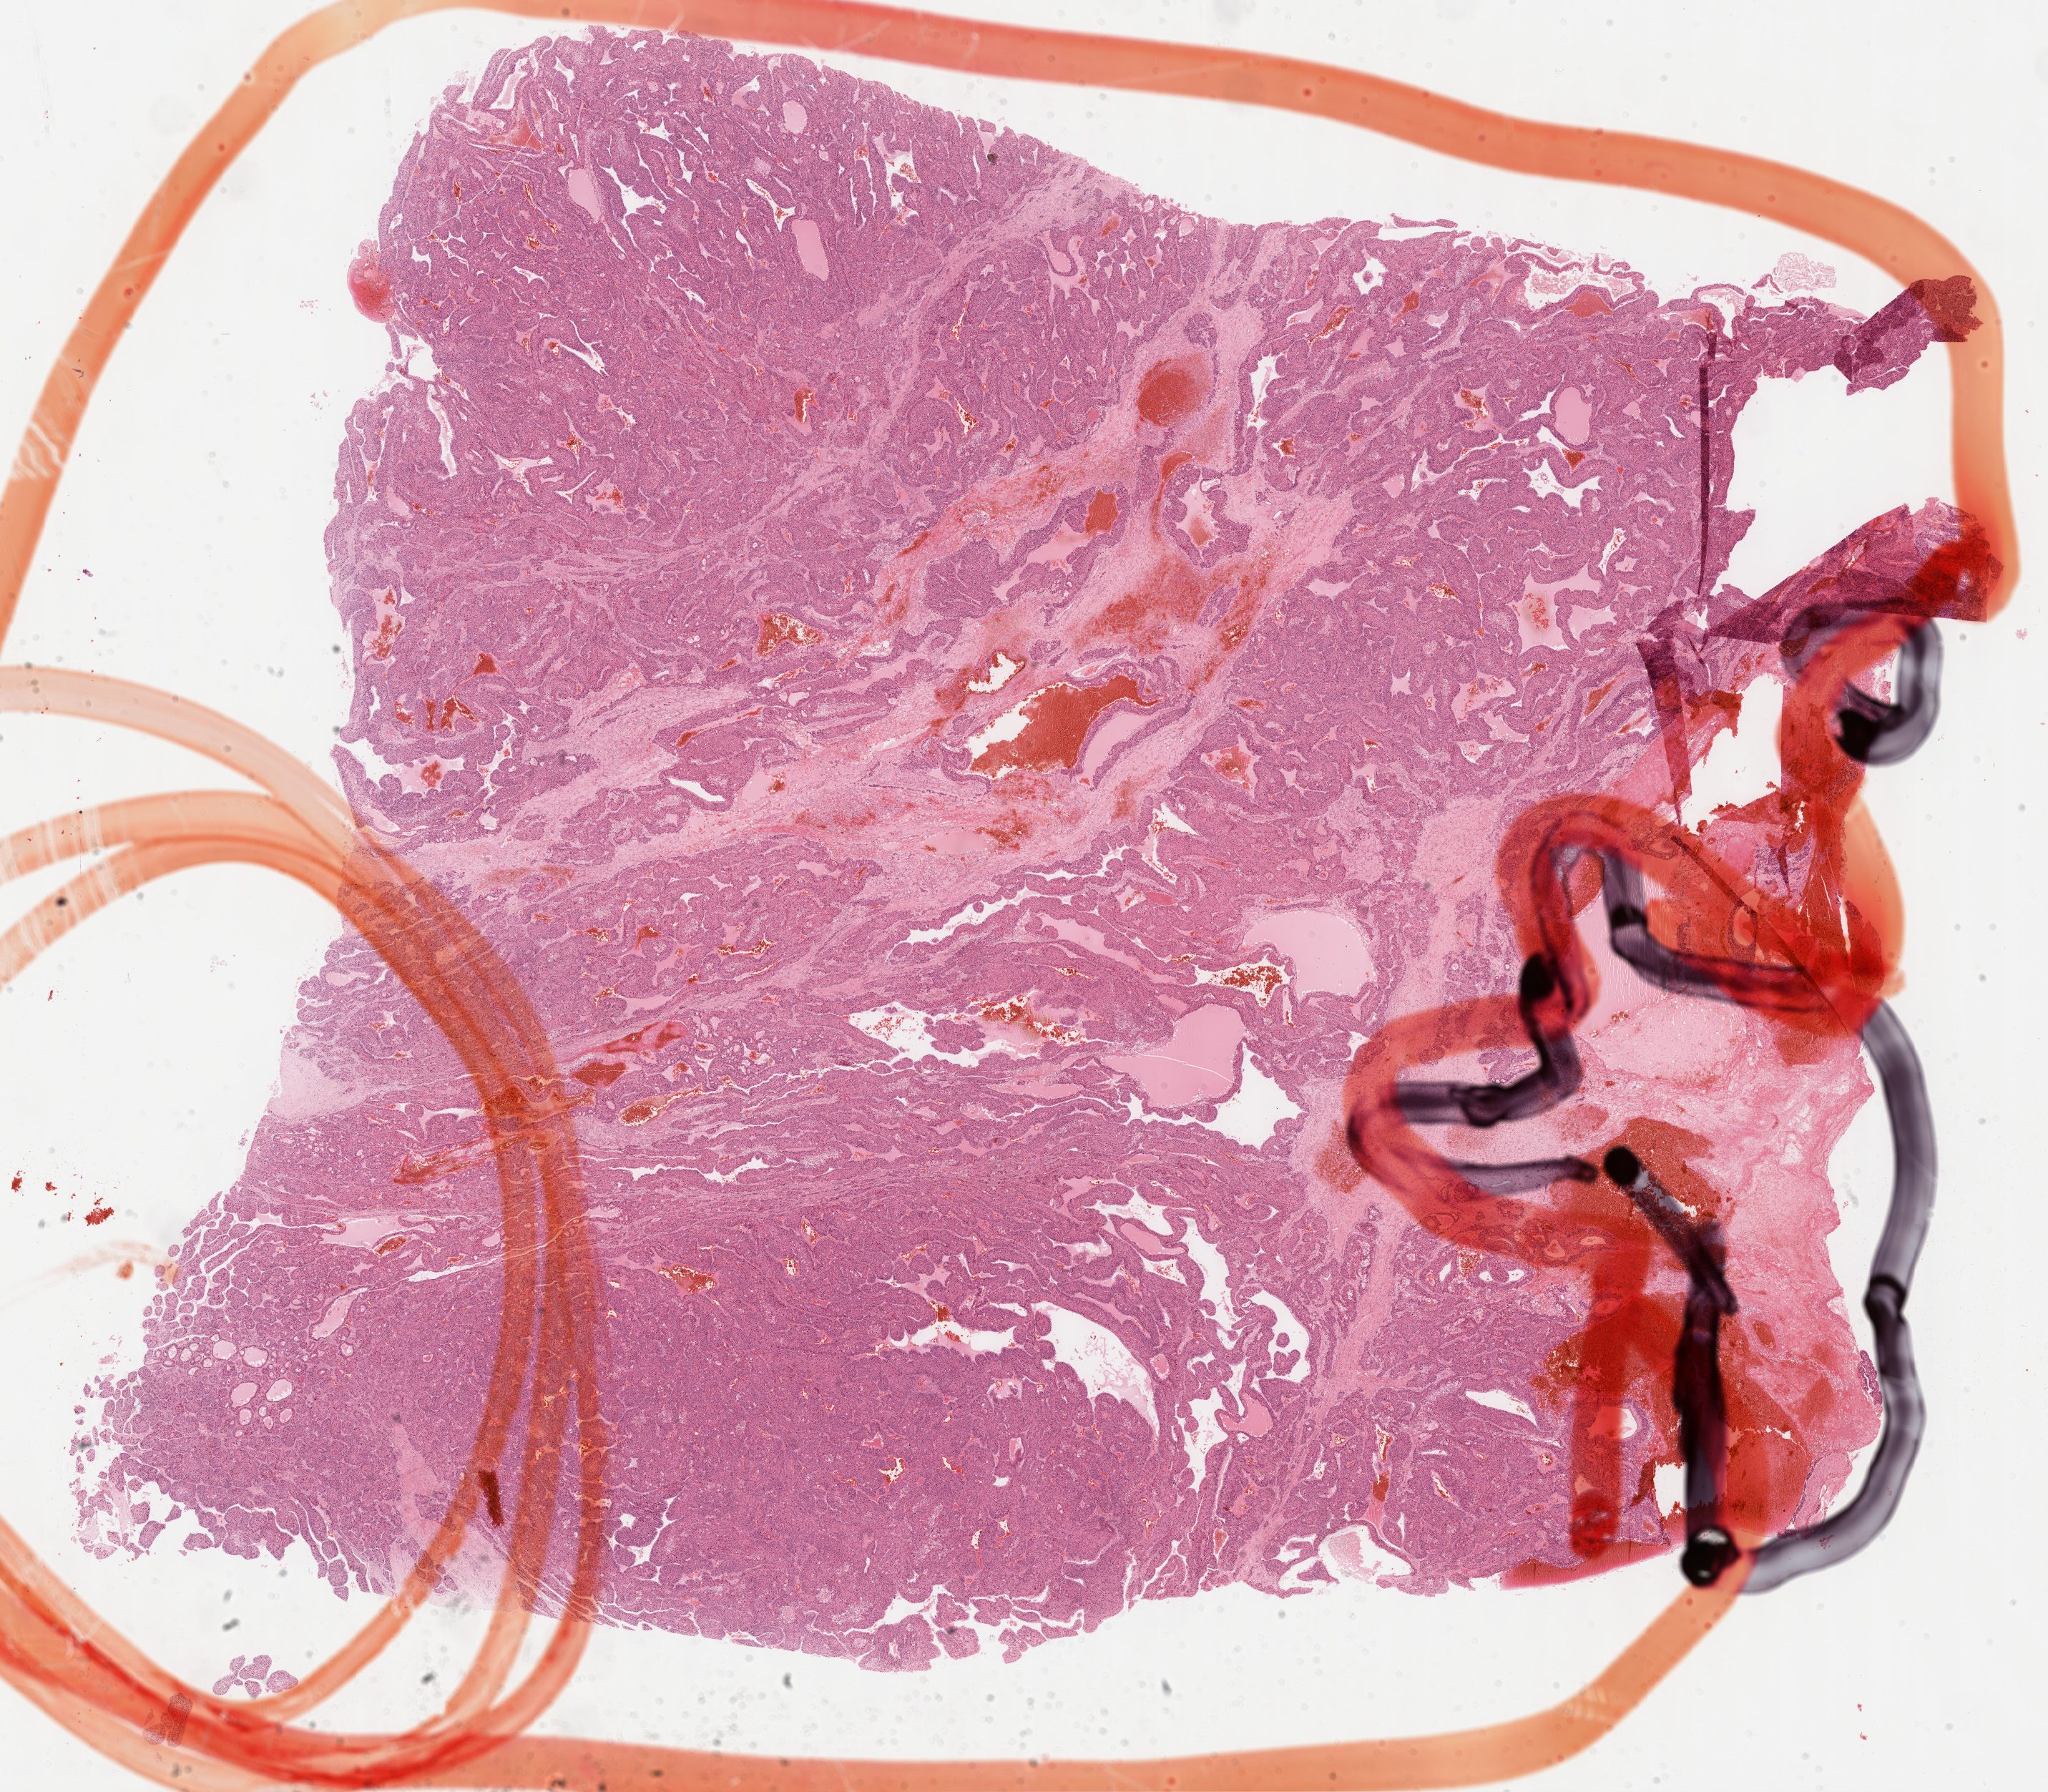
Whole-slide histology image, H&E-stained, whole scanned area (about 23.2 x 20.3 mm) shown as a low-resolution overview, formalin-fixed paraffin-embedded (FFPE) diagnostic section, sample: primary tumour, liver. Male patient; age at initial diagnosis 61 years. Histologic grade: G2 (moderately differentiated).
AJCC pathologic stage: II (7th edition). Diagnosis: Hepatocellular carcinoma, NOS.